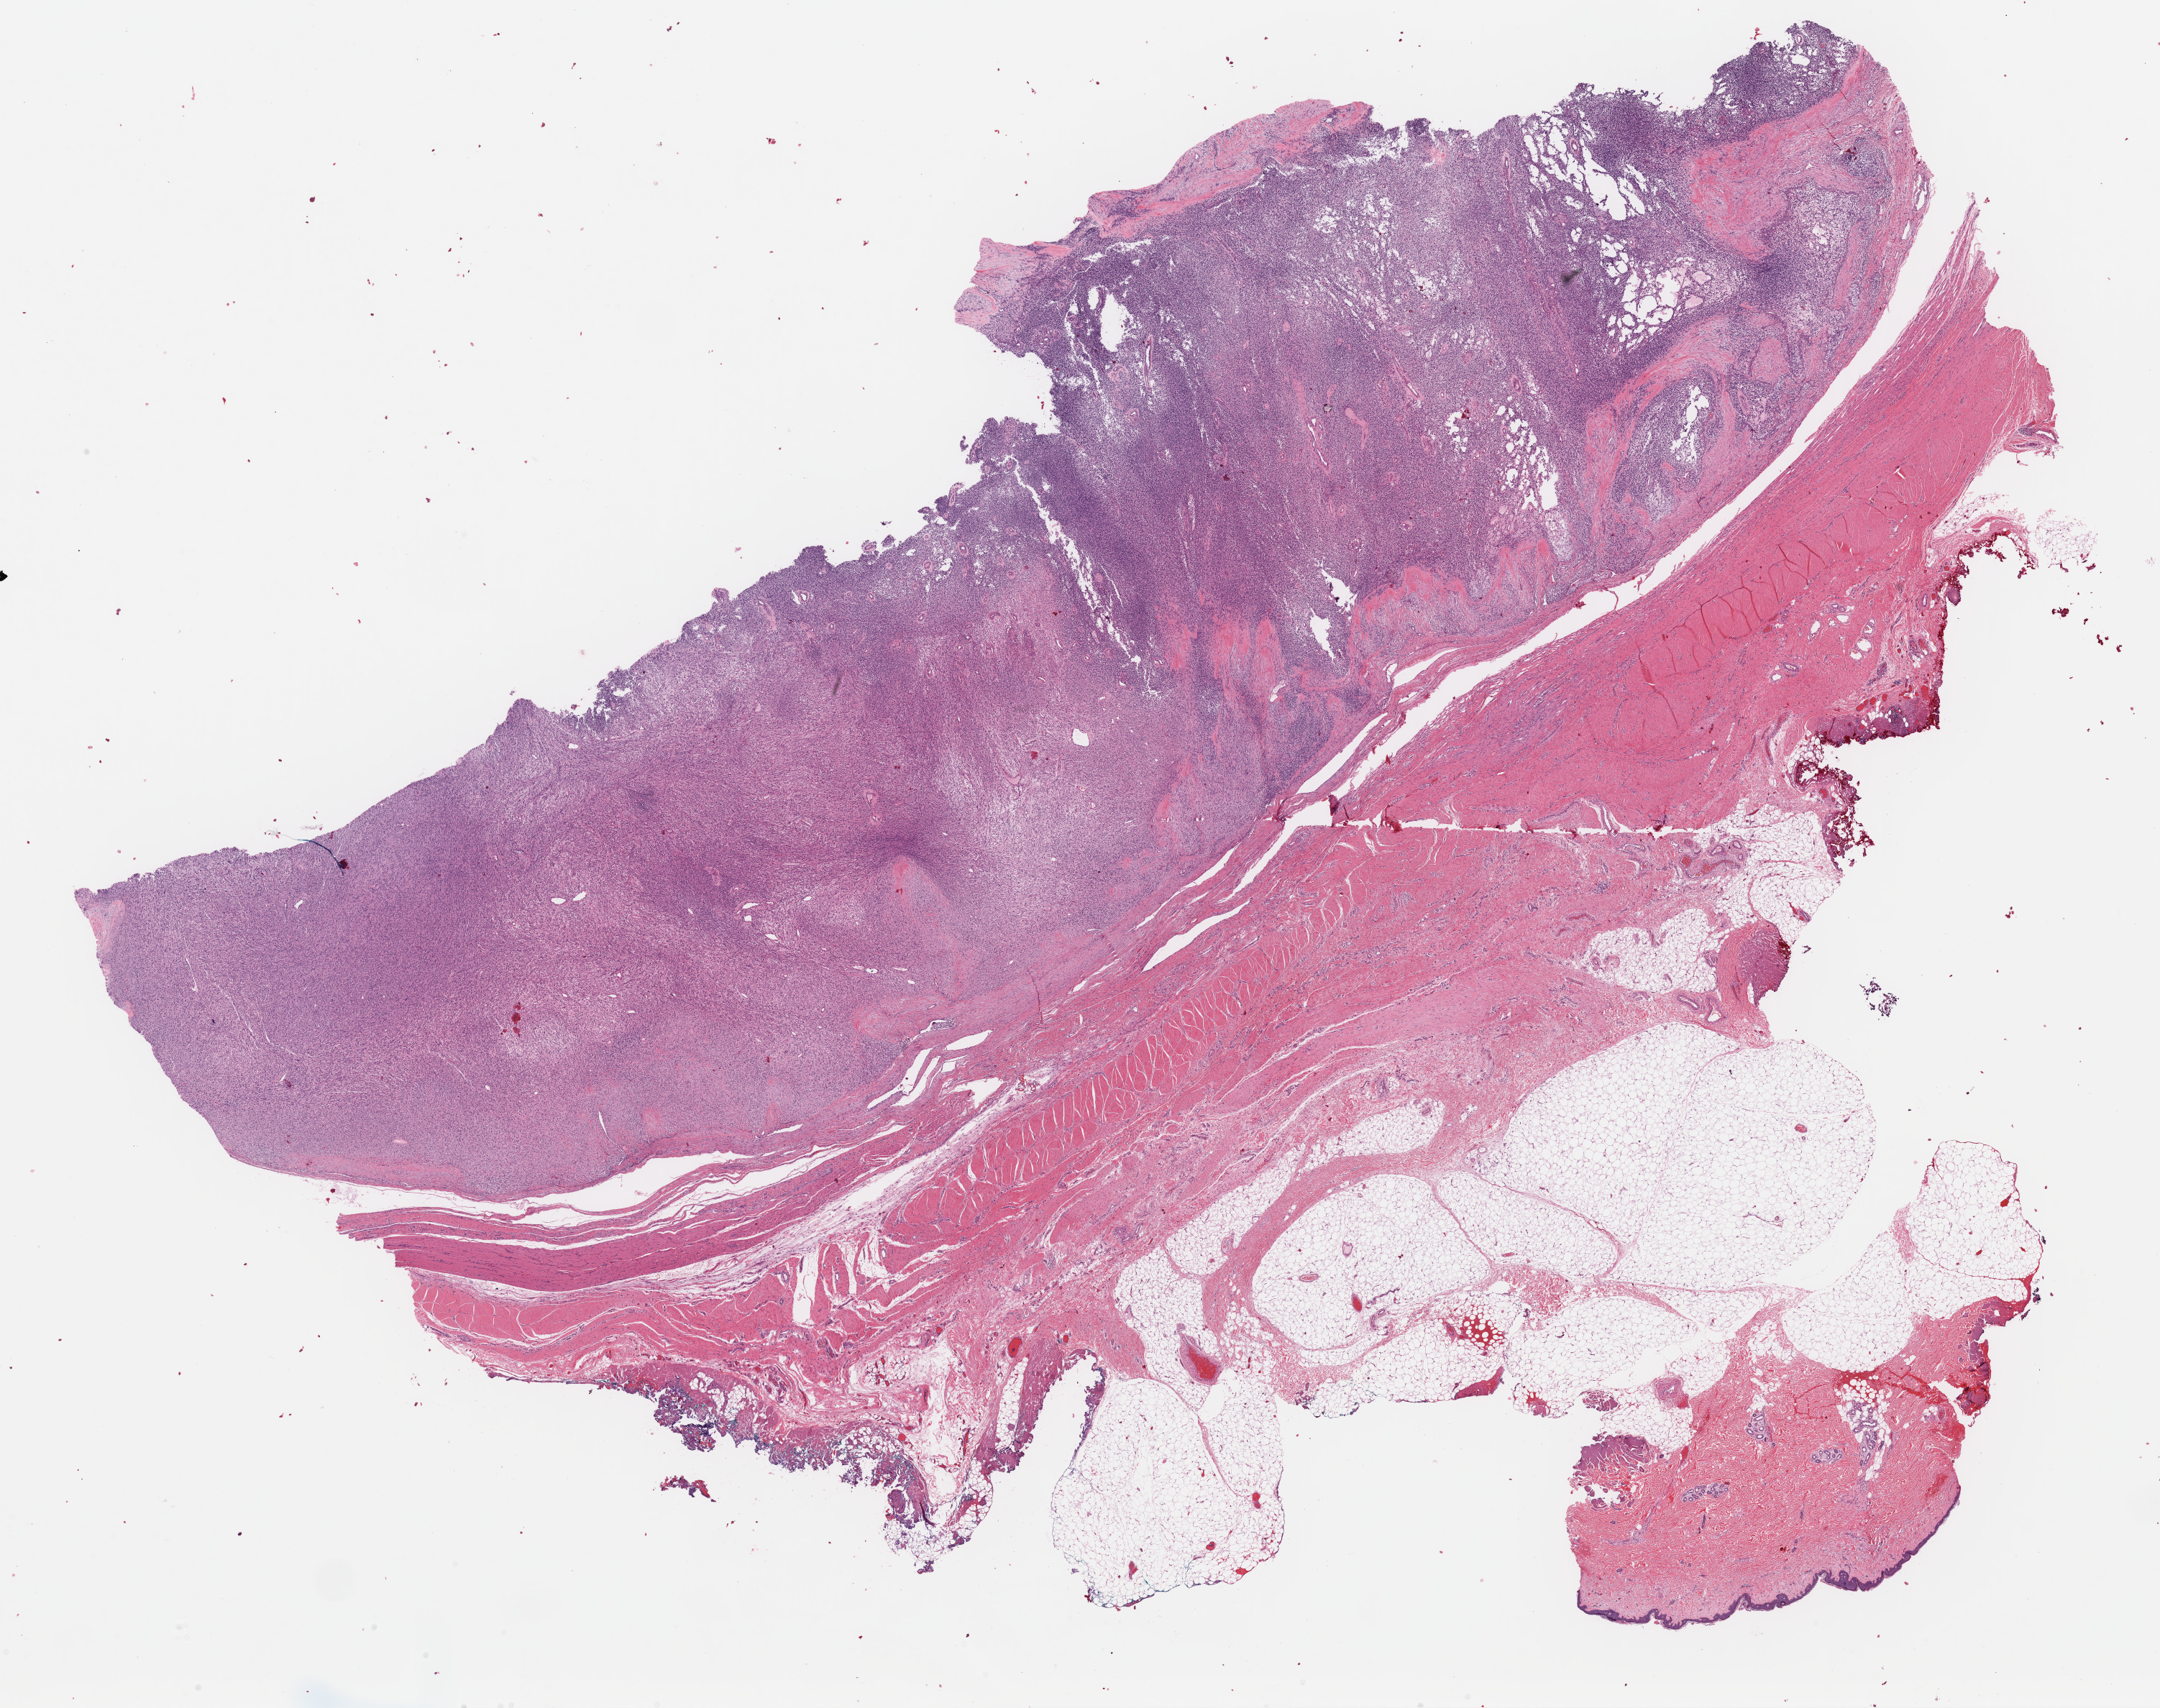
Whole-slide histology image, Hematoxylin and eosin (H&E) stained — shown as a low-resolution overview of the whole scanned area (about 23.7 x 18.8 mm), formalin-fixed paraffin-embedded (FFPE) diagnostic section, metastatic tumour sample. Male patient; age at initial diagnosis 50 years.
• this section: metastatic tumour tissue
• patient diagnosis: Malignant melanoma, NOS